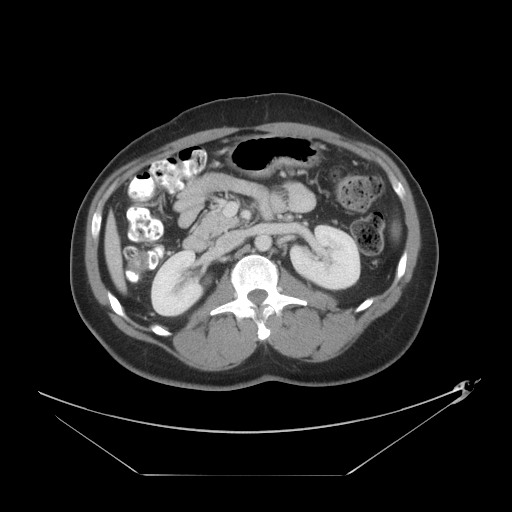
Contrast-enhanced abdominal CT, one axial slice. Position 17 of 44 along the scan axis. Reconstruction kernel STANDARD. 120 kVp. Soft-tissue window (W 400 / L 40 HU). 5 mm slice thickness. 512 × 512 image matrix, field of view 466 × 466 mm. Male patient, age 49 years. Case-level facts recorded for this patient, not image findings: diagnosis: colorectal cancer liver metastases, imaged before liver resection; multiple liver metastases: no; largest metastasis: 8.5 cm; disease in both lobes: yes.
Annotated regions visible in this slice (outlined manually by an expert reader):
- liver: bounding box <105,215,125,289> (left, top, right, bottom; pixels)